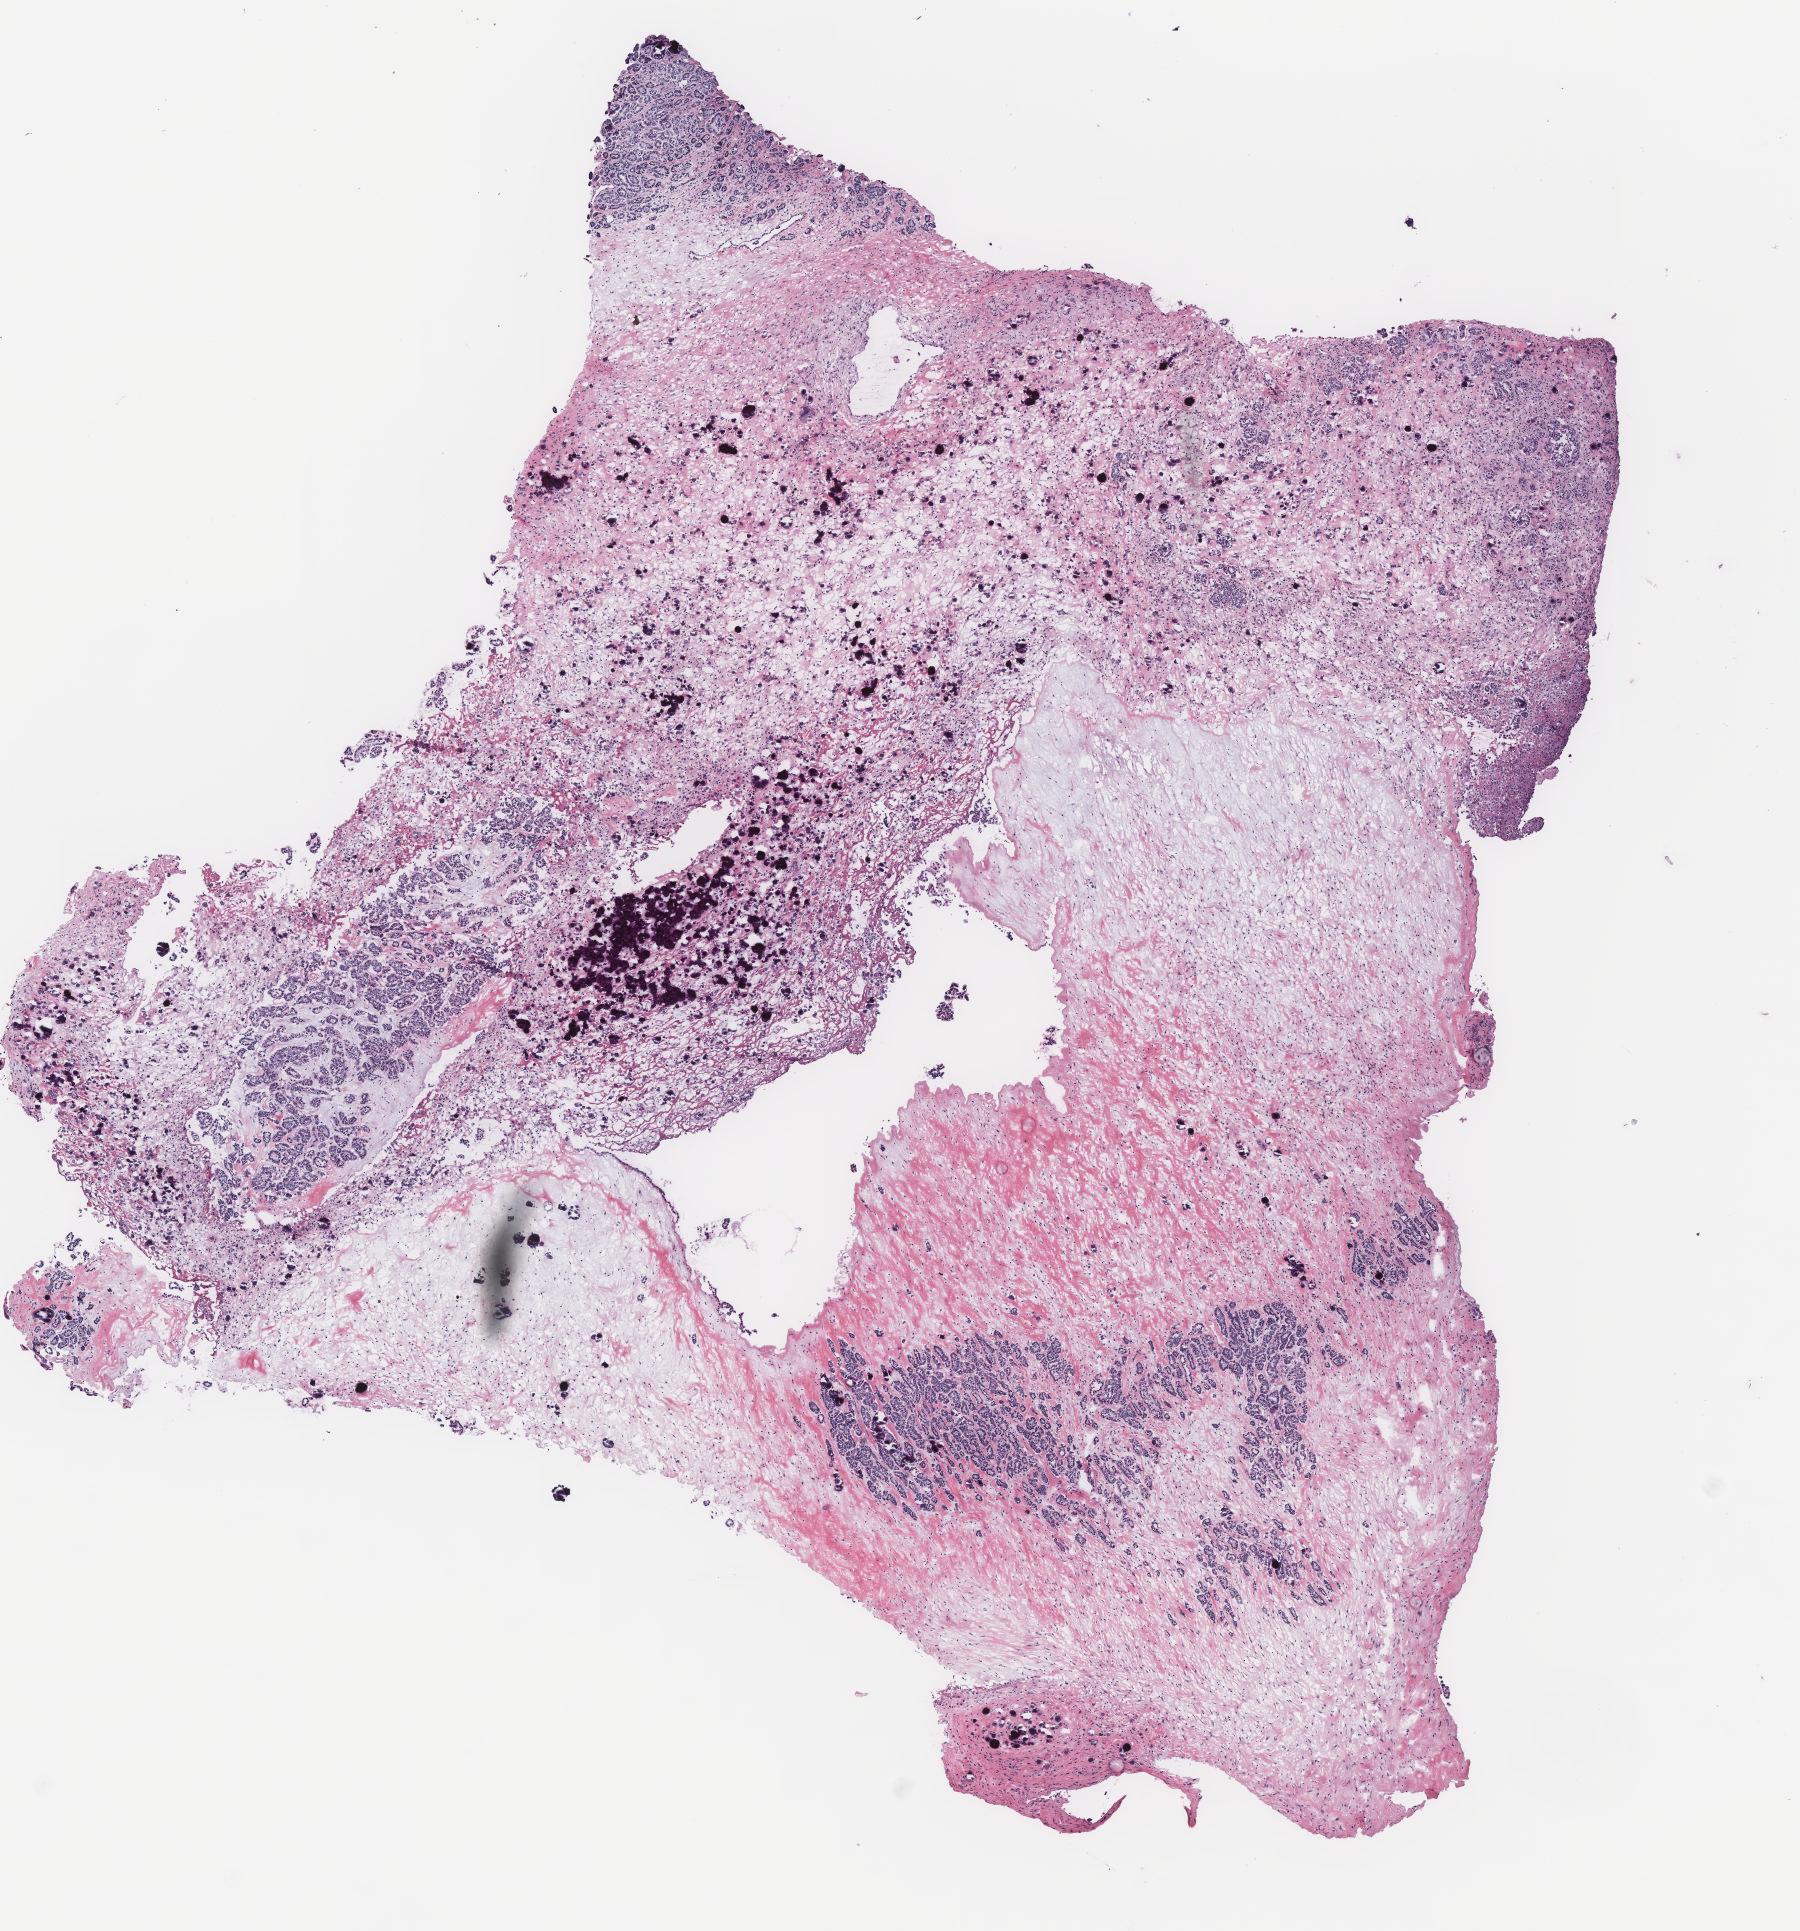
H&E whole-slide image, low-resolution overview of the scanned area, about 7.2 x 7.7 mm (from a 40x scan); tumour tissue sample, ovary. 57-year-old female patient.
* diagnosis: Serous adenocarcinoma, NOS
* primary tumour site (as recorded): ovary